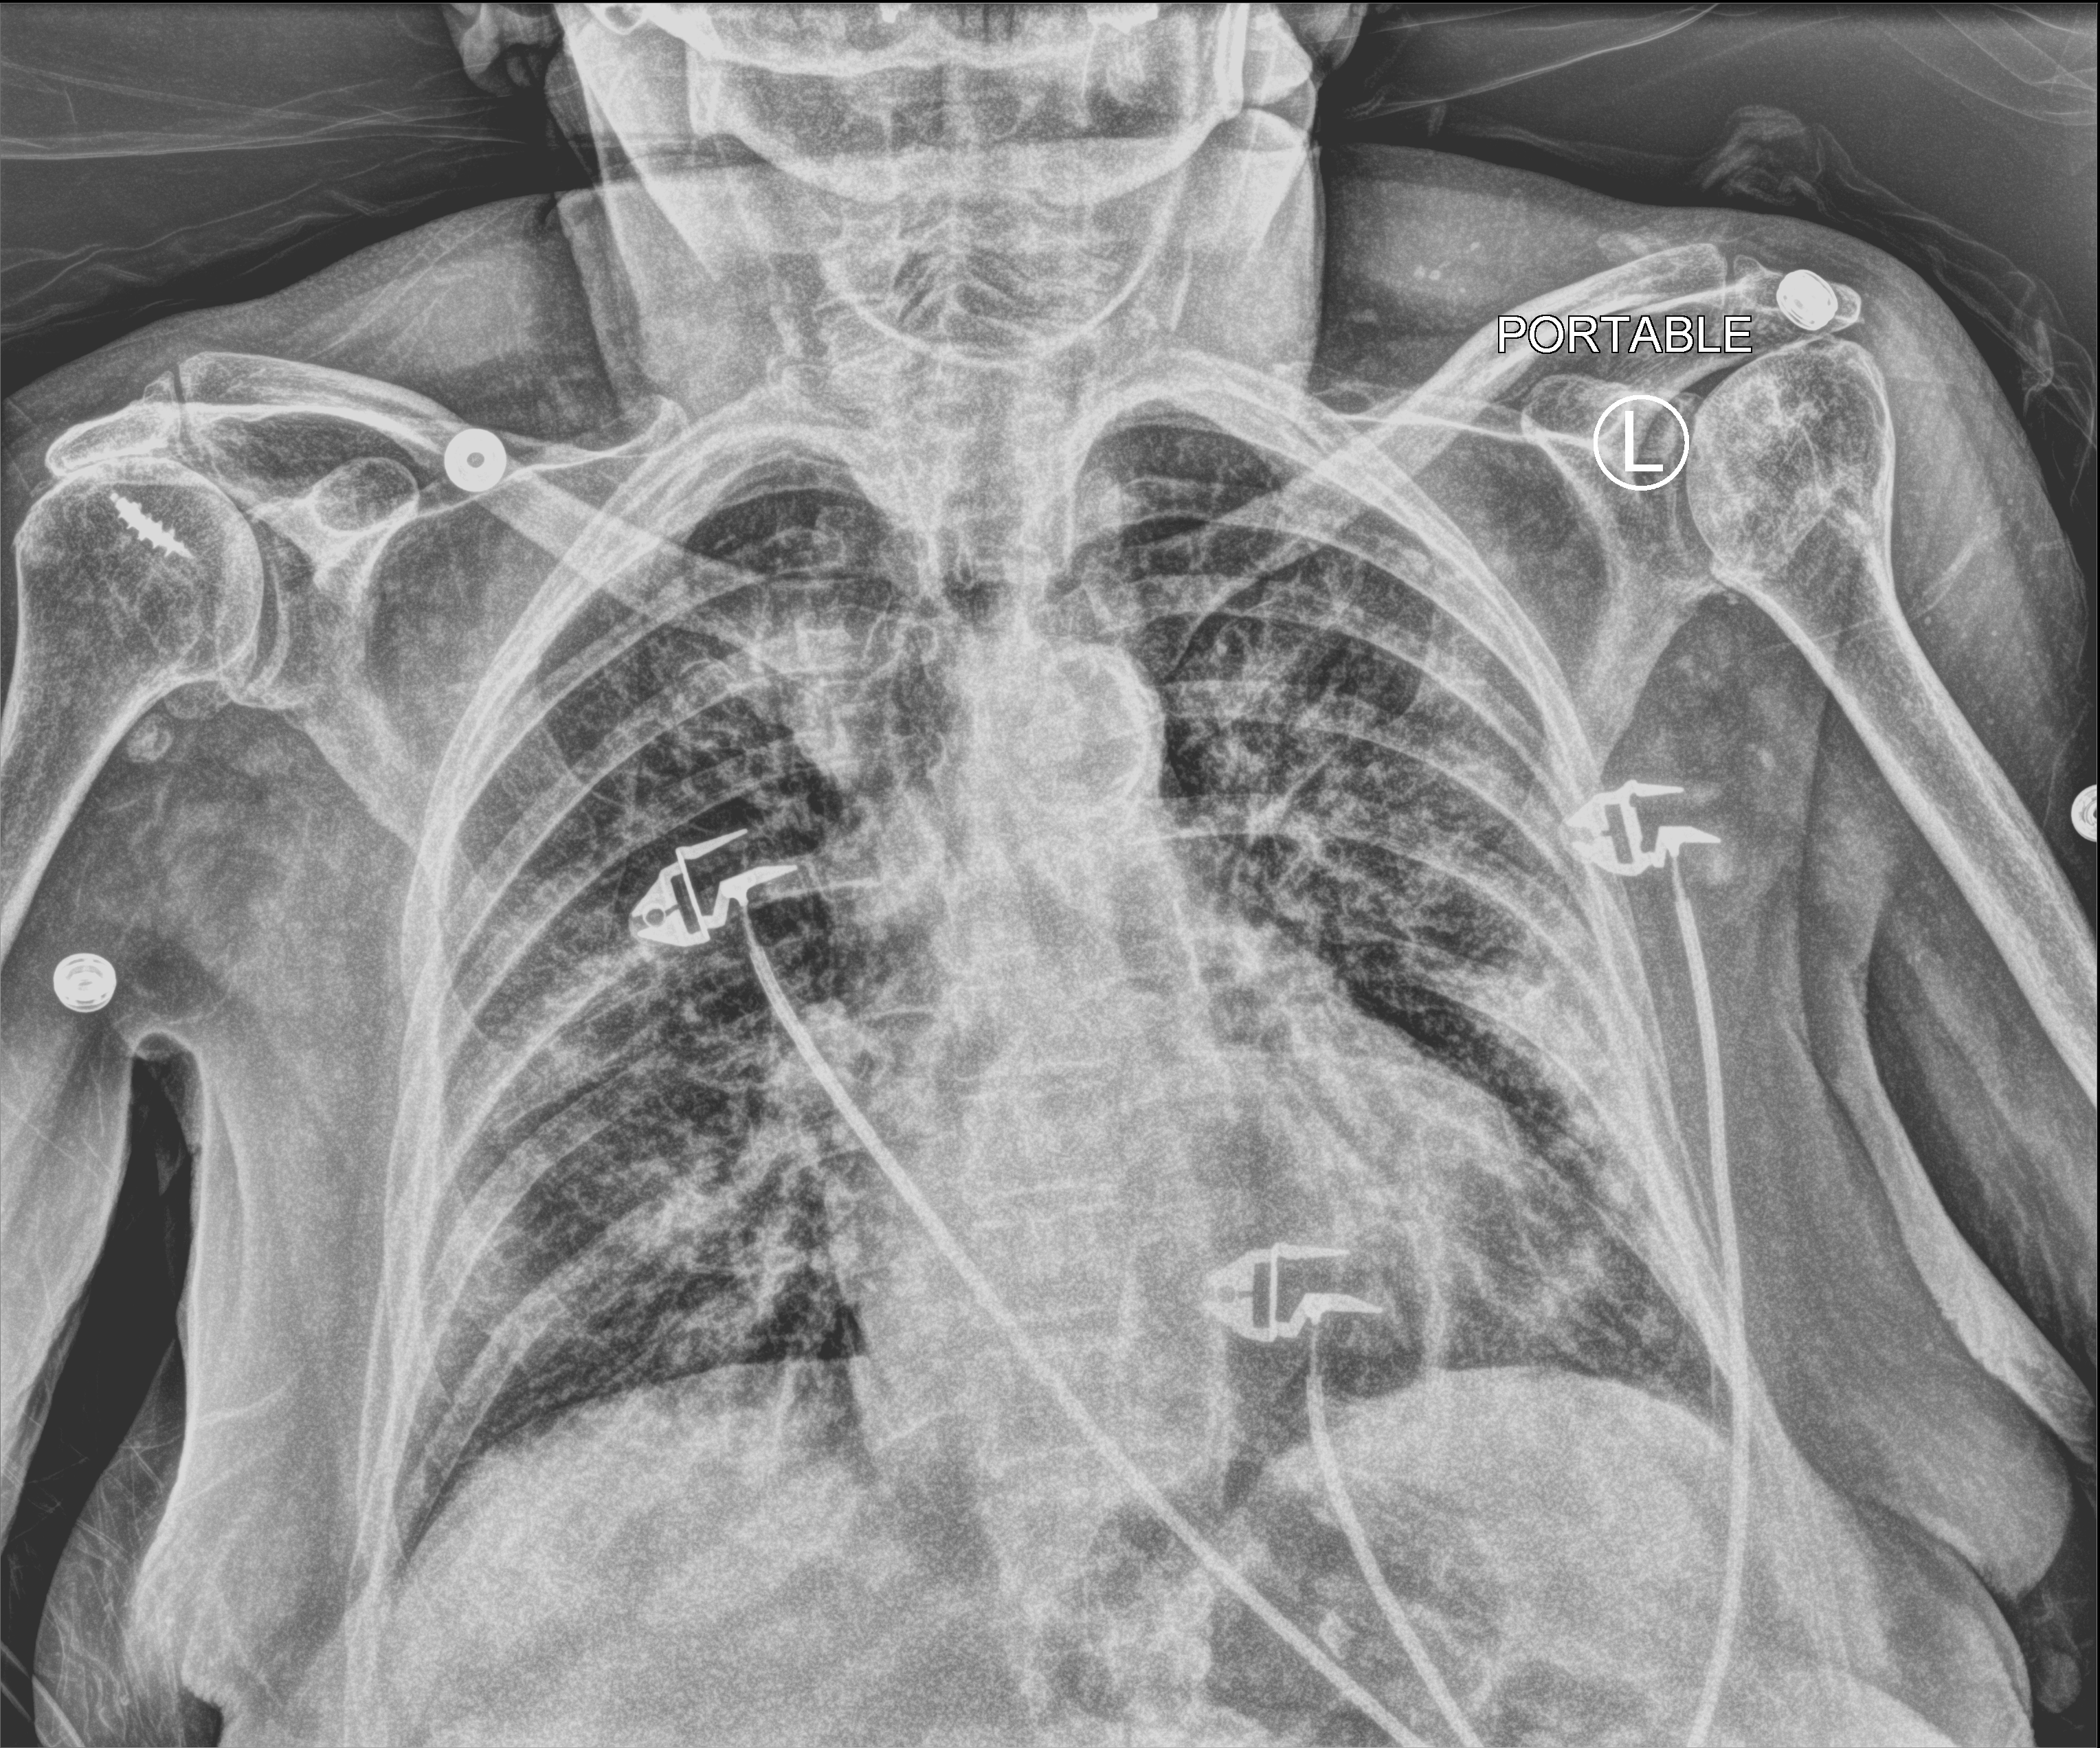
Chest X-ray (portable), anteroposterior (AP) projection. Female patient hospitalised with COVID-19, age 75–90 years.
Hospital-stay facts (about this admission, not read from this image; timing relative to this image not recorded):
- mechanically ventilated during this hospital stay: no